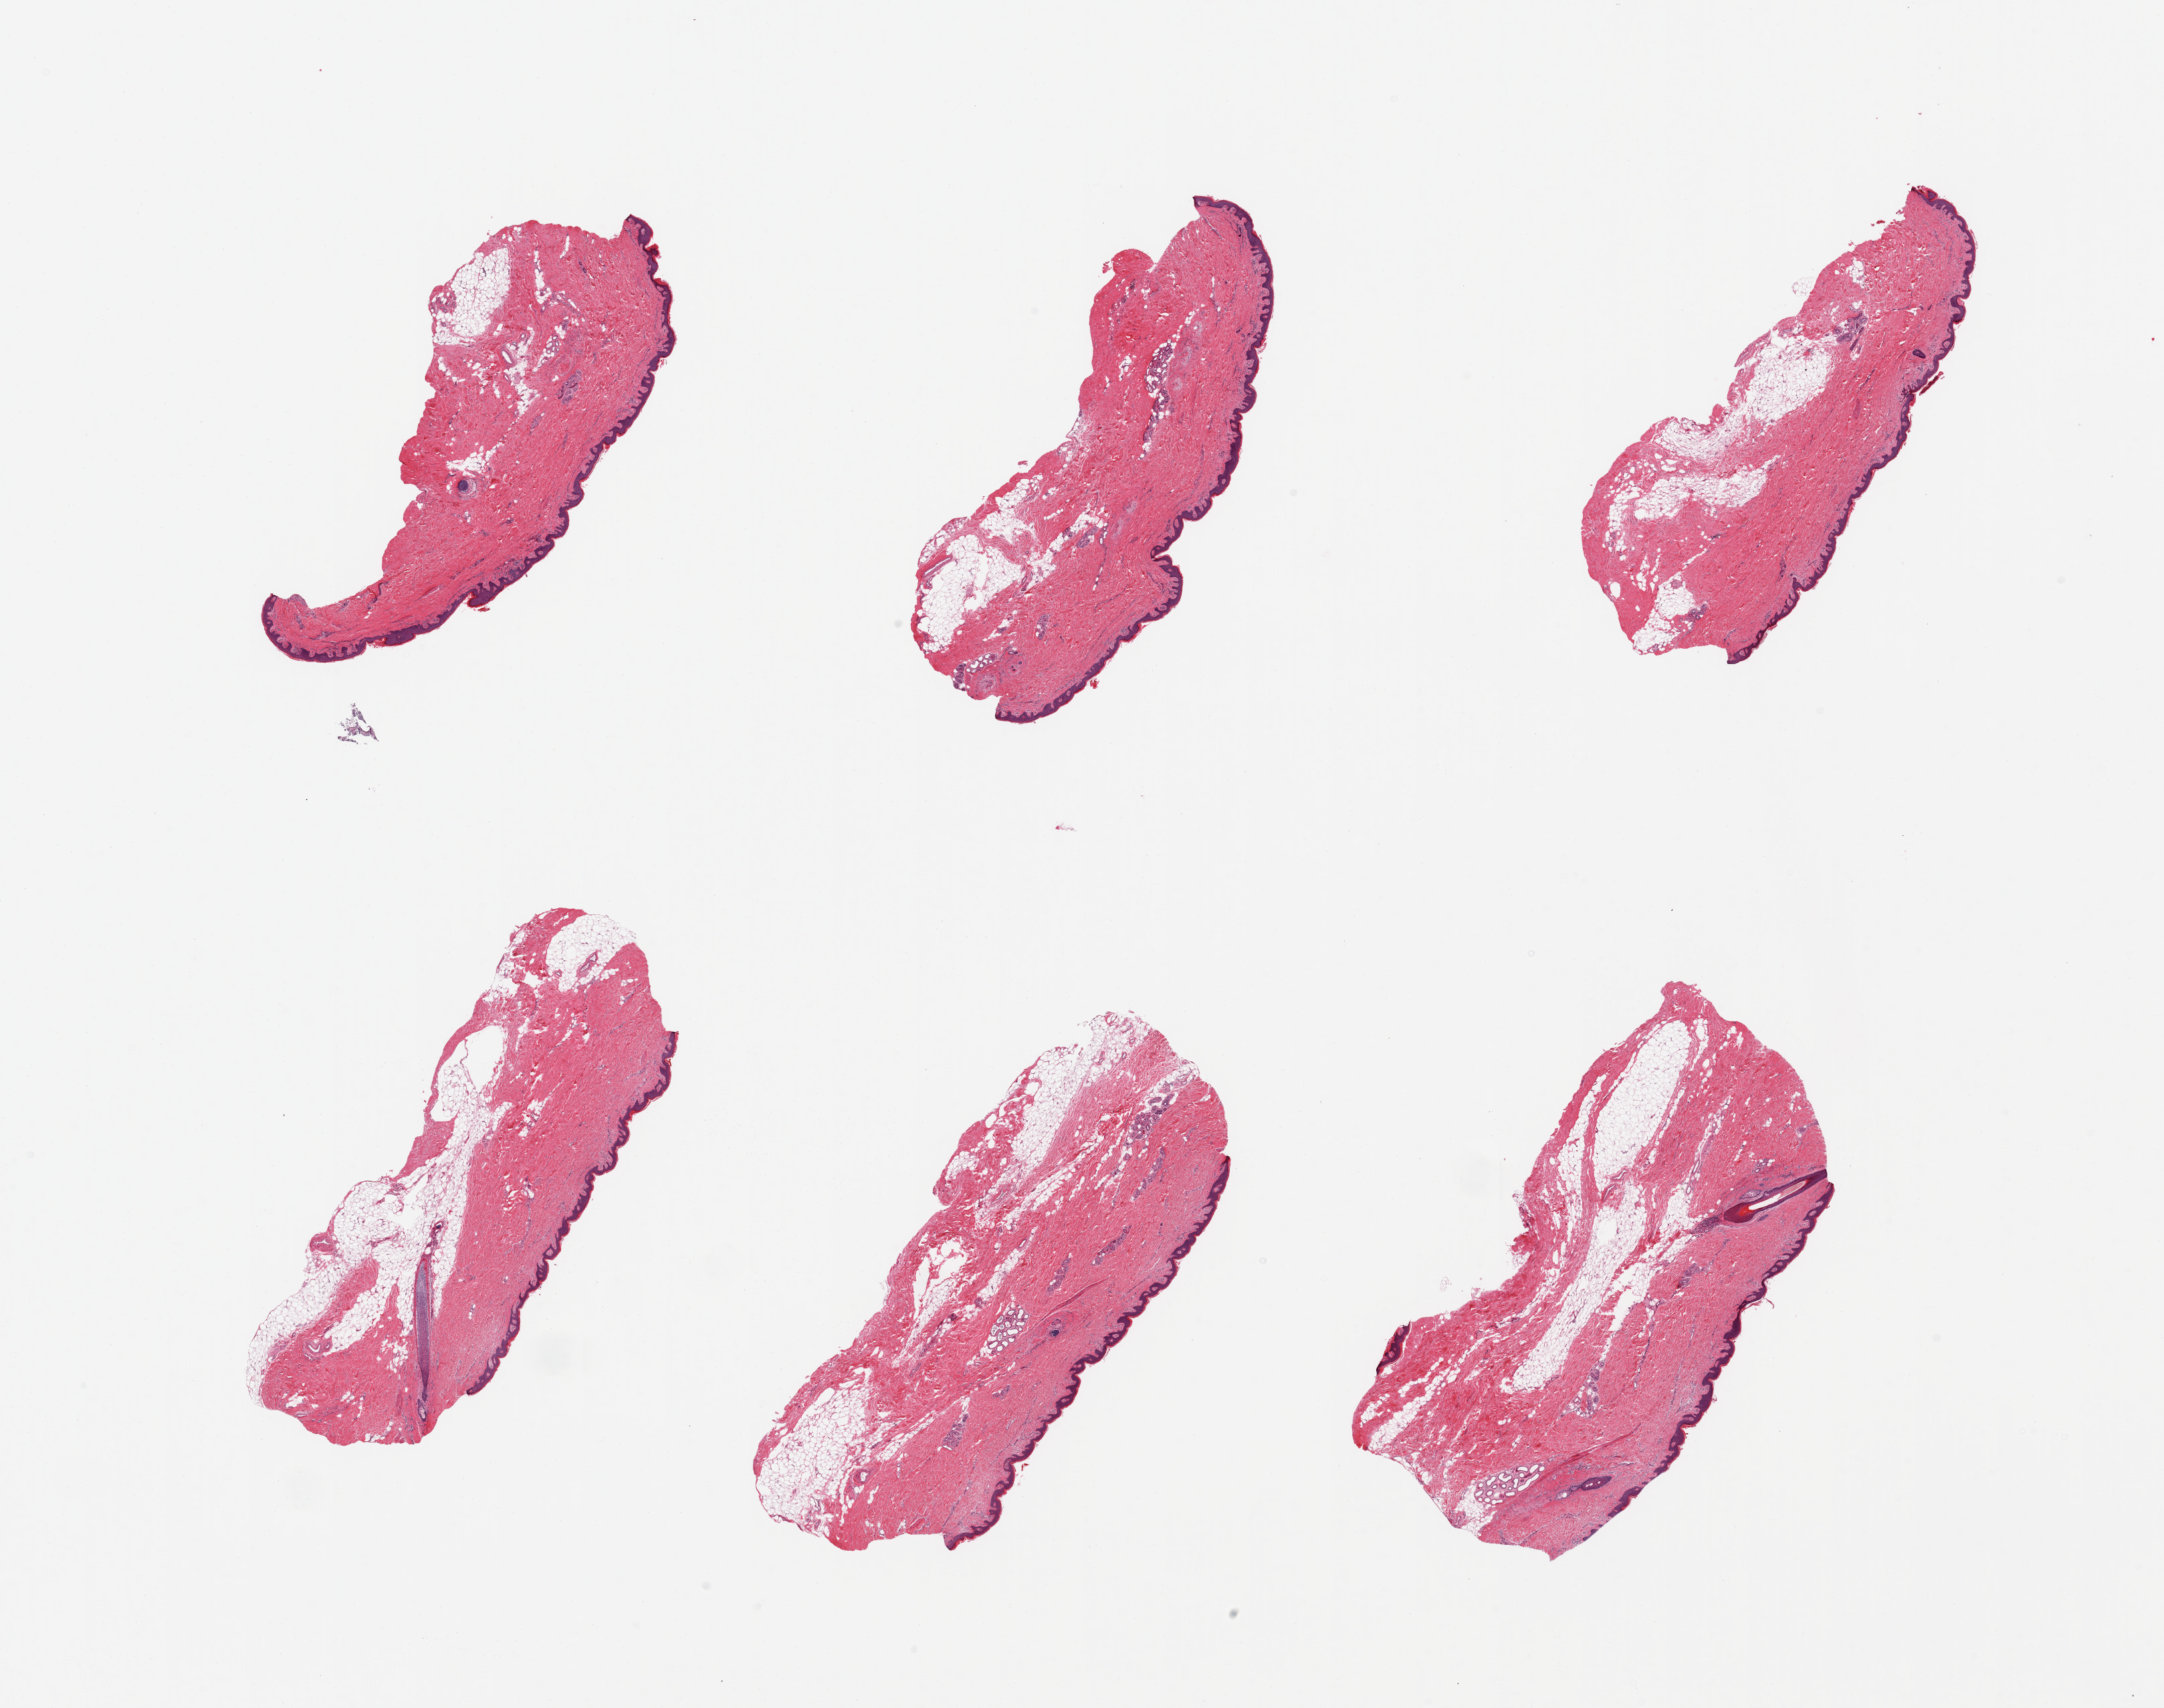
Hematoxylin and eosin (H&E) whole-slide image — shown as a low-resolution overview of the whole scanned area (about 25.6 x 20.2 mm, from a 20x scan). PAXgene-fixed, paraffin-embedded tissue. Section of skin of suprapubic region (target tissue). Donor tissue sample. Female donor.
Review note (as recorded): 6 pieces, squamous epithelium is ~70 microns; adherent dermal fat up to ~1mm.